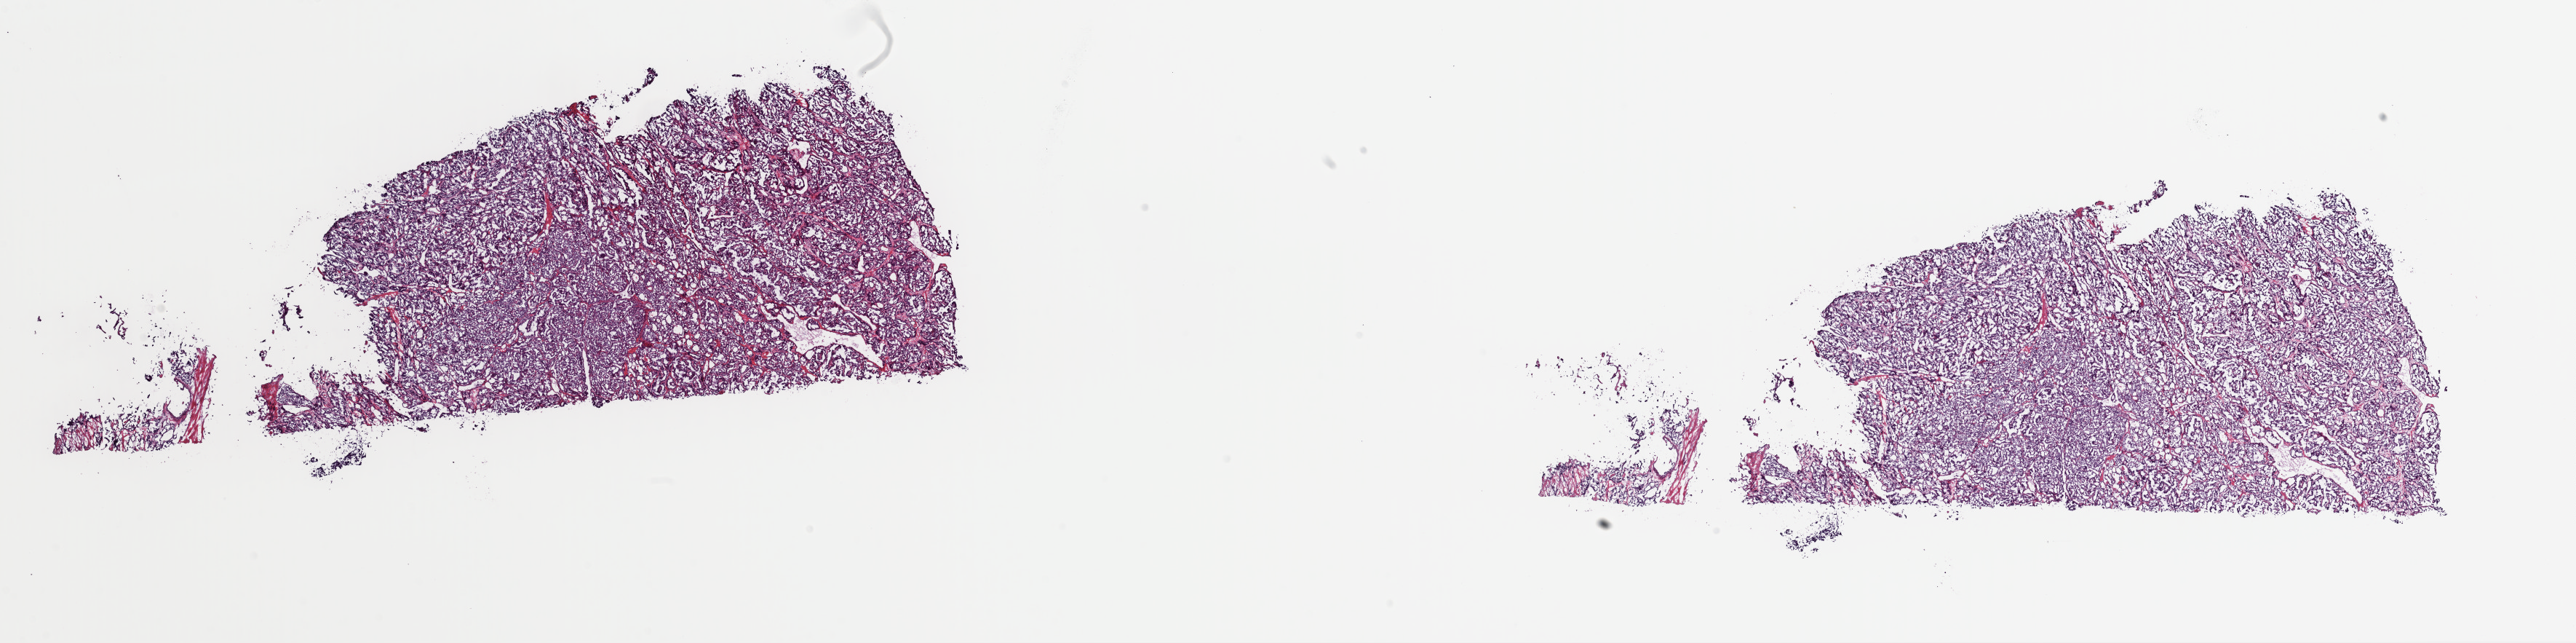
Hematoxylin and eosin (H&E) stained whole-slide image — low-resolution overview of the scanned area, about 28.0 x 7.0 mm (acquisition: 40x scan), frozen section from the top of the tissue portion, thyroid, primary tumour sample. Male patient; age at initial diagnosis 31 years. Composition of this section per pathologist review: tumour cells 90%, tumour nuclei 100%, normal cells 0%, stromal cells 10%, necrosis 0%. Infiltration values recorded for this section: lymphocyte infiltration 0%, monocyte infiltration 0%, neutrophil infiltration 0%.
* lymph nodes positive (case pathology): 3 of 3 examined
* AJCC pathologic stage: I (7th edition)
* pathologic diagnosis: Papillary adenocarcinoma, NOS (thyroid gland)